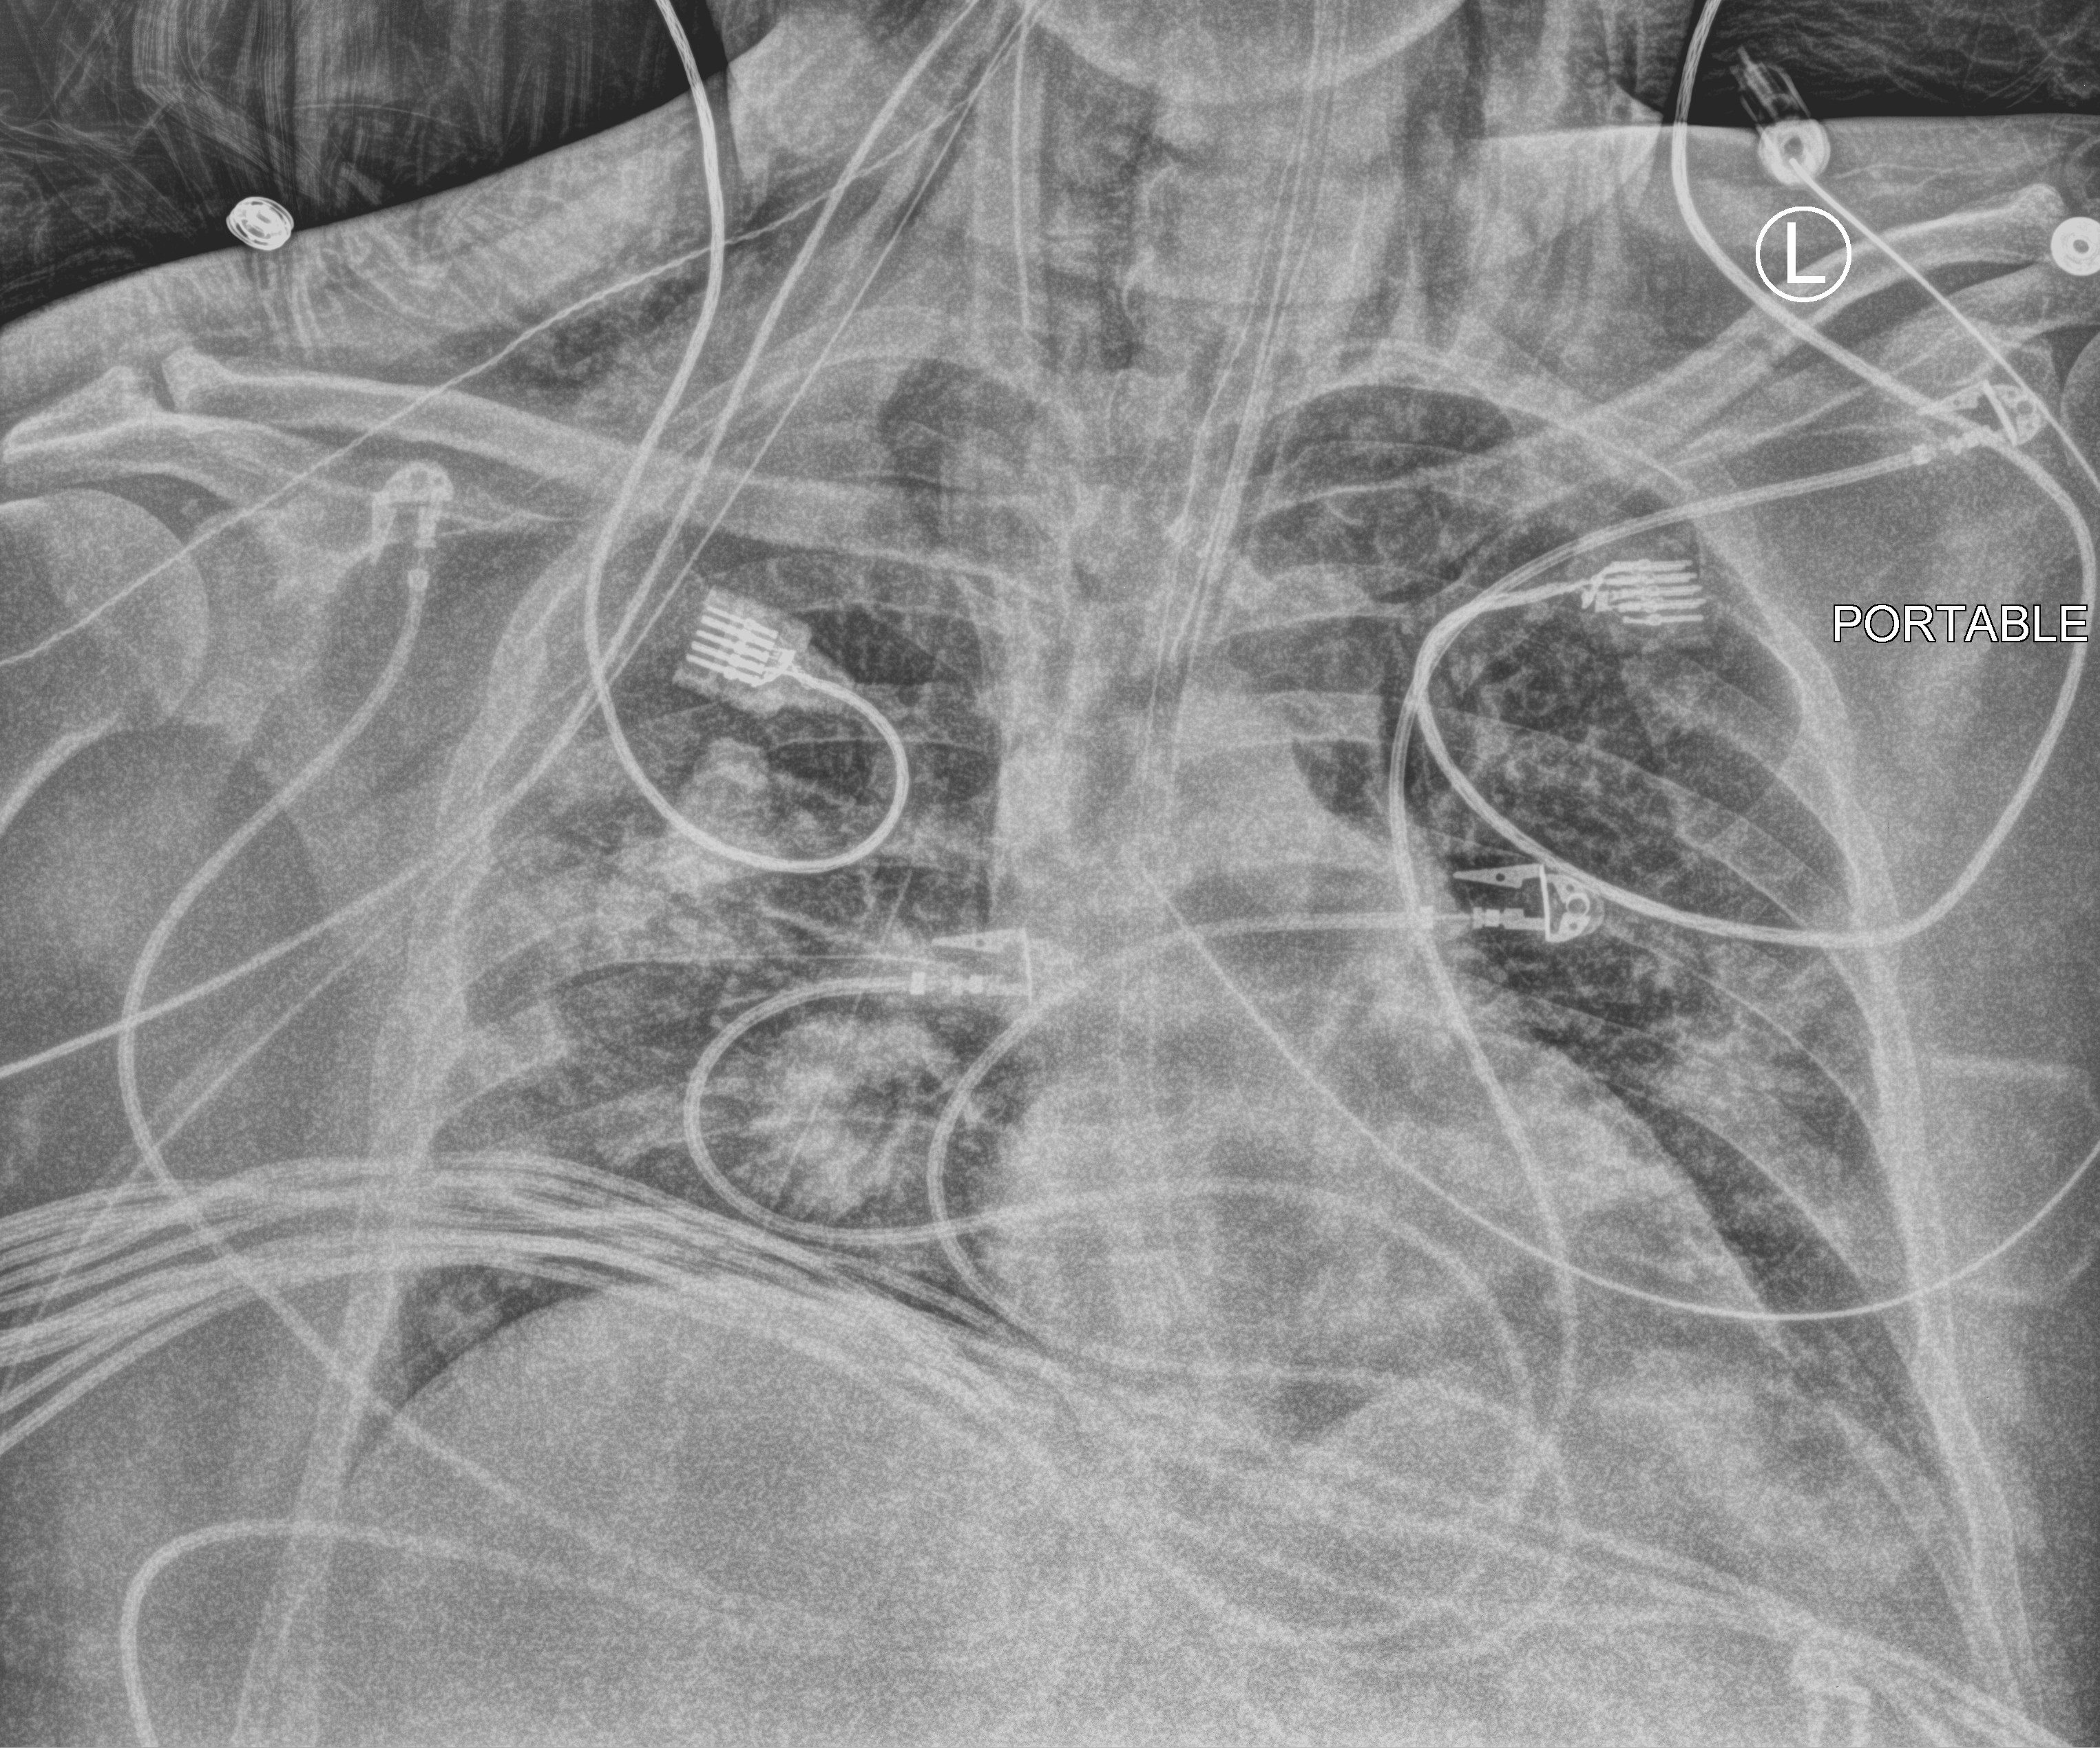
Chest X-ray (portable); anteroposterior (AP) projection. Patient hospitalised with COVID-19, aged 18–59 years.
From the hospital-stay record, not from the radiograph (when in the stay this image was taken is not recorded): COPD (admission record): no; diabetes (admission record): no.